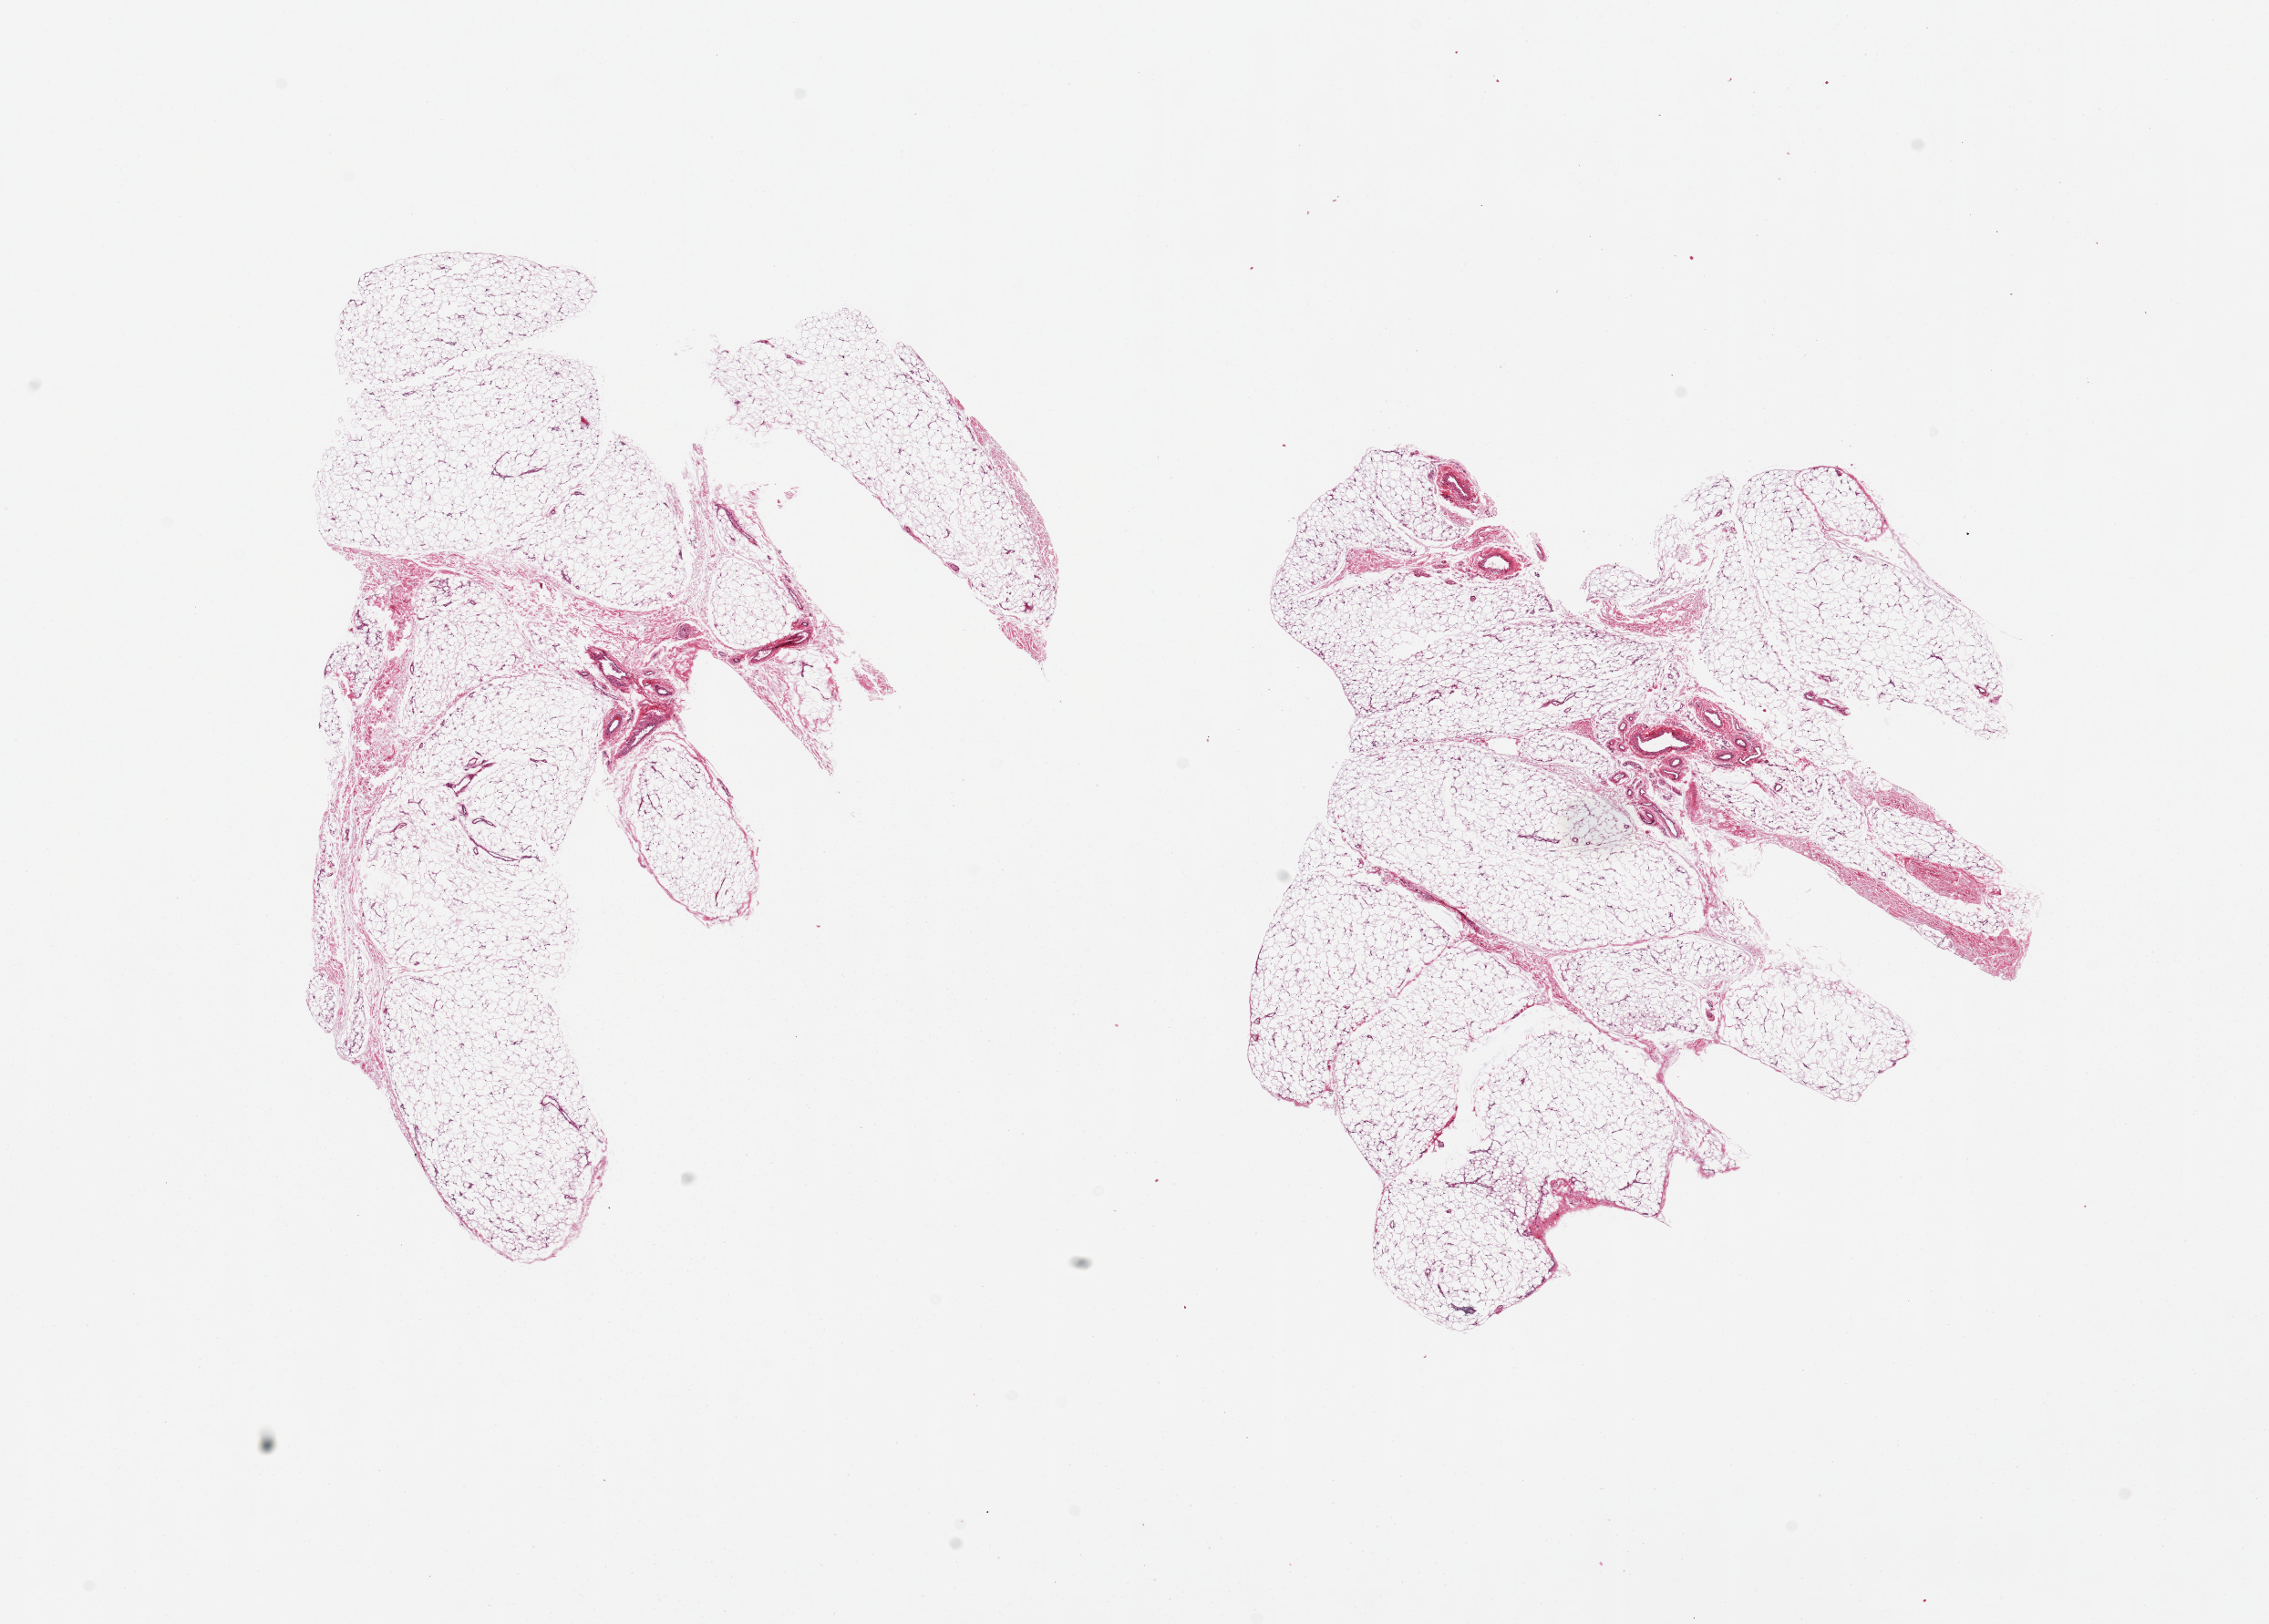
Digitized H&E-stained section, brightfield, whole scanned area (about 19.7 x 14.1 mm) shown as a low-resolution overview. PAXgene-fixed paraffin-embedded (PFPE) section. Target tissue: adipose tissue. Tissue donor sample. Donor: male.
* review note (as recorded): 2 pieces 8x7 & 7.5x6.5 mm; good fixation